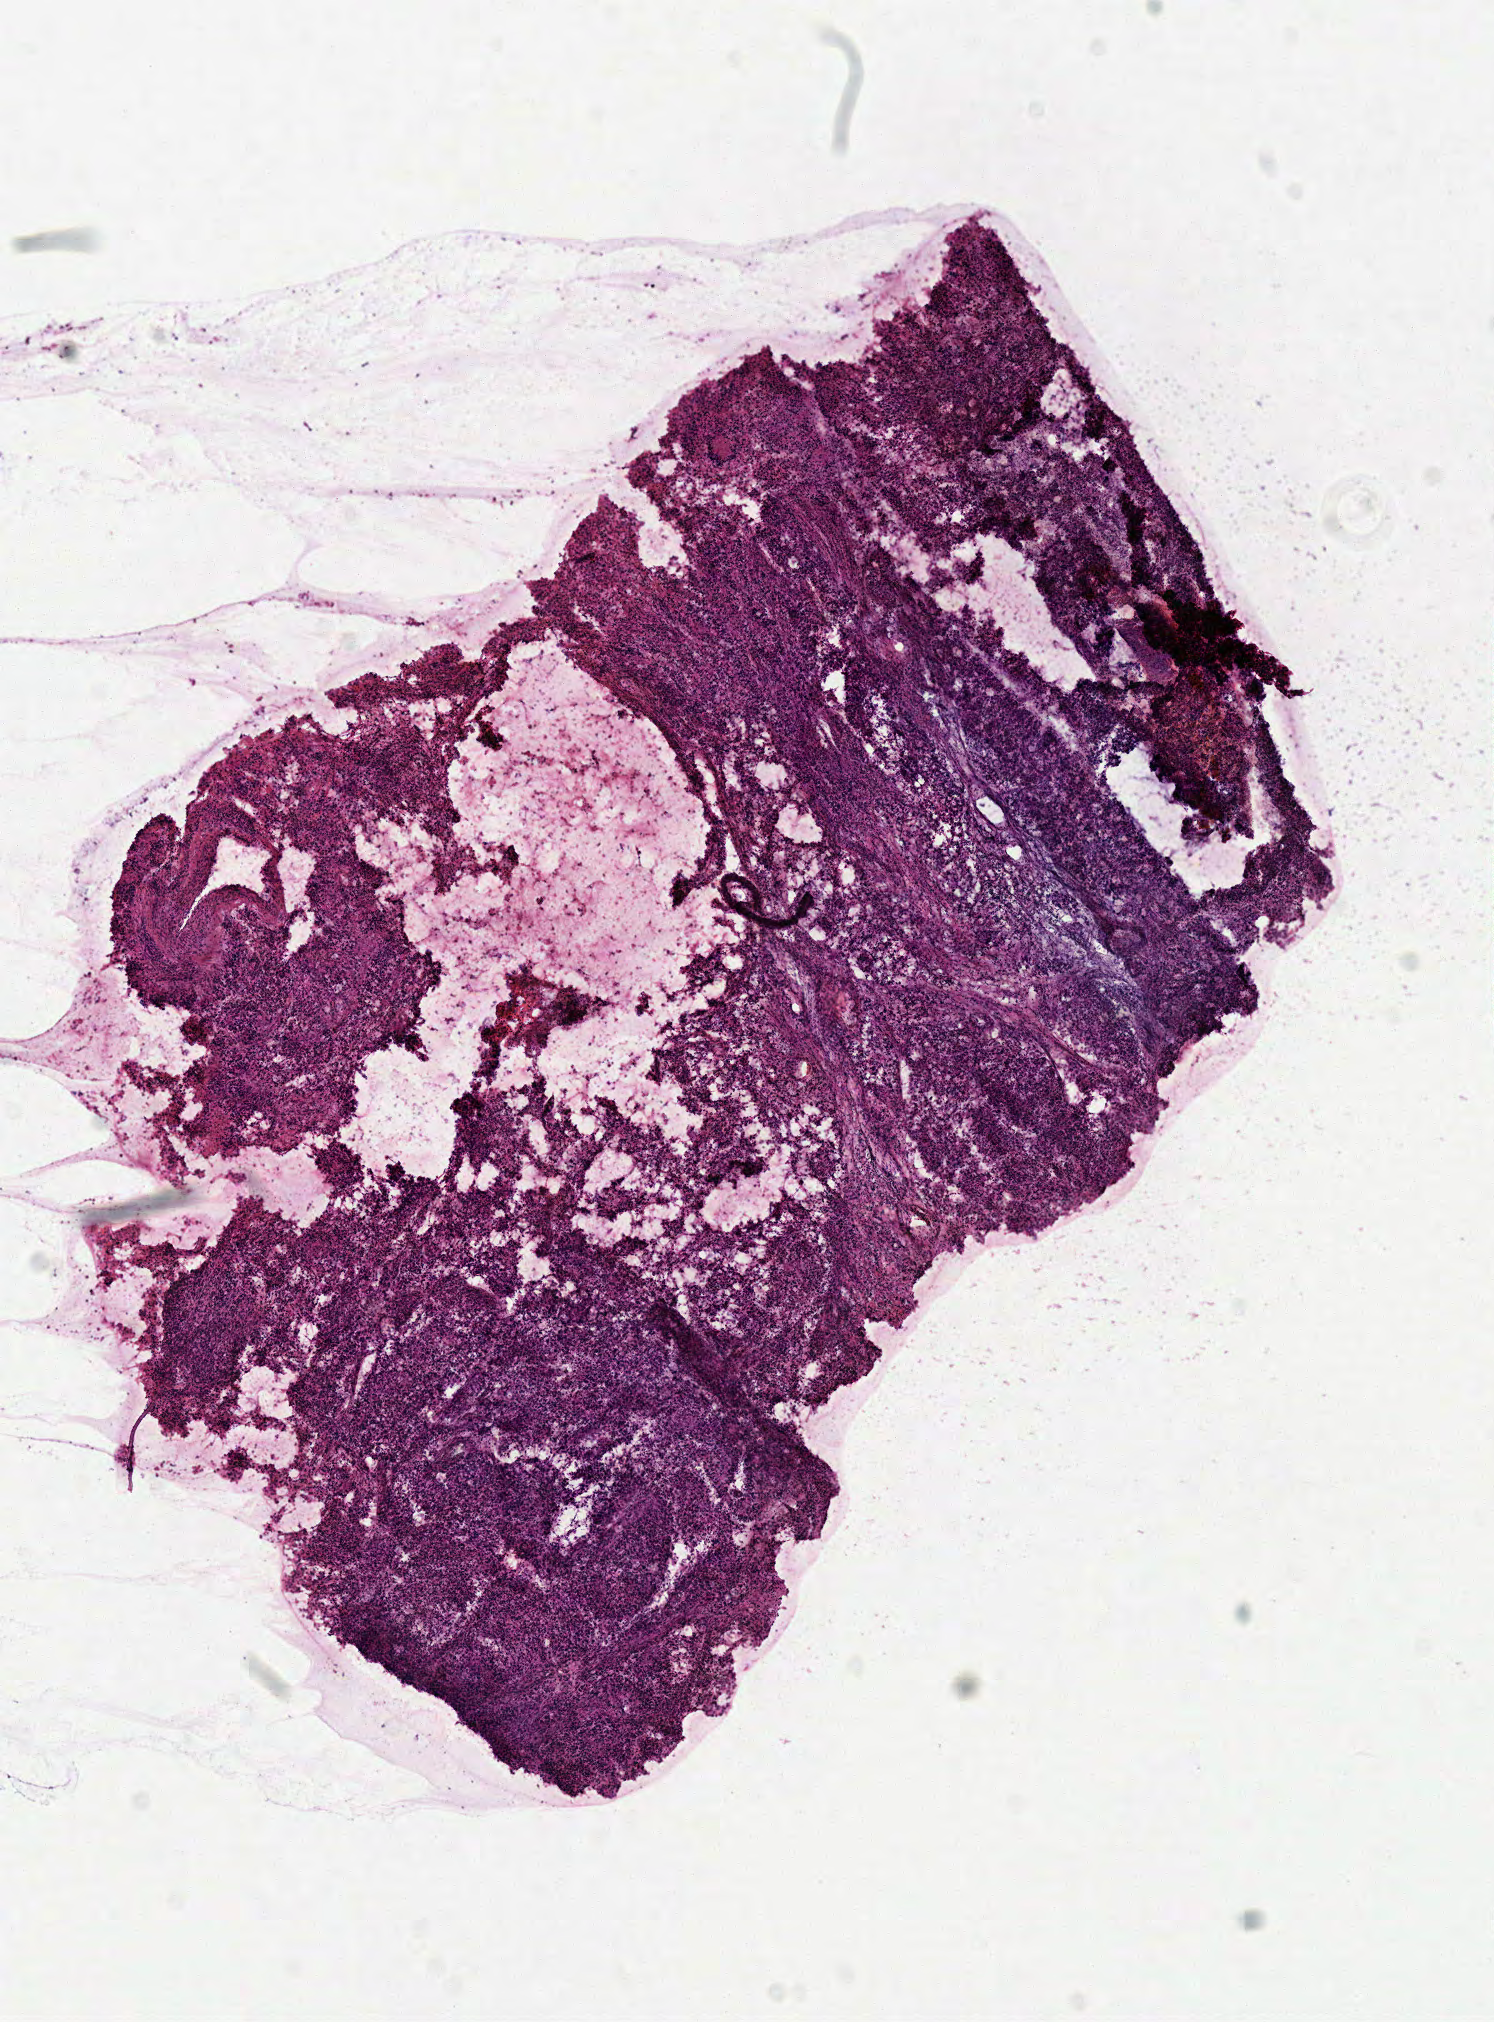
Digitized Hematoxylin and eosin (H&E) stained tissue section (whole slide), shown as a low-resolution overview of the whole scanned area (about 5.9 x 7.9 mm, slide scanned at 40x); frozen section from the top of the tissue portion; brain, primary tumour sample. Male, age 57 years at initial diagnosis. Slide review estimates, as recorded: tumour cells 80%, tumour nuclei 75%, normal cells 0%, stromal cells 15%, necrosis 5%.
Diagnosis: Glioblastoma.